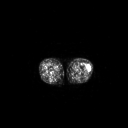
FDG PET of an extremity soft-tissue mass (from a PET/CT study), one axial slice; slice 180 of 223 in the series (ordered by position); 3.27 mm slice thickness; 128 × 128 image matrix, field of view 700 × 700 mm. Female patient, age 16 years. Case-level facts recorded for this patient, not image findings: histological type: spindle cell suggestive of biphasic synovial sarcoma; grade: intermediate; site of the primary tumour: left knee.
Structures marked on this image (expert contour drawn on MRI and transferred to this co-registered scan by the dataset authors):
- gross tumour volume including surrounding oedema: bounding box [x1, y1, x2, y2] px = [86, 63, 91, 70]
- gross tumour volume (mass): [86, 63, 91, 70]